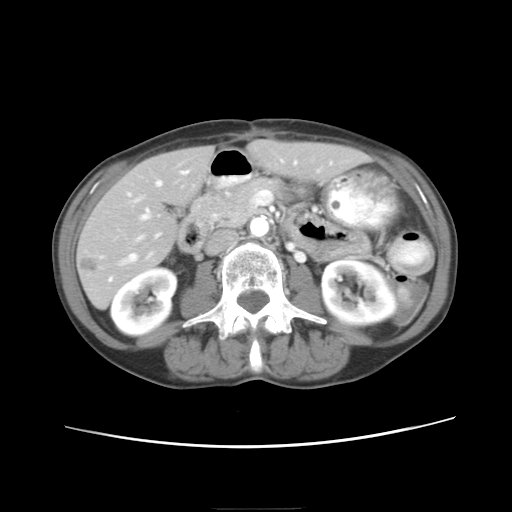
Contrast-enhanced abdominal CT, one axial slice. Slice 7 of 26 in the series (ordered by position). 120 kVp. Intravenous contrast given. Soft-tissue window (W 400 / L 40 HU). 512 × 512 image matrix, field of view 340 × 340 mm. Female patient, age 65 years. From the clinical record (not read from this slice): diagnosis: colorectal cancer liver metastases, imaged before liver resection; multiple liver metastases: no.
Structures marked on this image (expert manual segmentation):
- hepatic veins: bounding box [x1, y1, x2, y2] px = [119, 170, 319, 265]
- liver: [77, 143, 362, 306]
- planned liver remnant (the part of the liver to remain after resection): [82, 143, 362, 306]
- portal vein (with intrahepatic branches): [128, 160, 296, 239]
- liver metastasis: [78, 254, 105, 273]